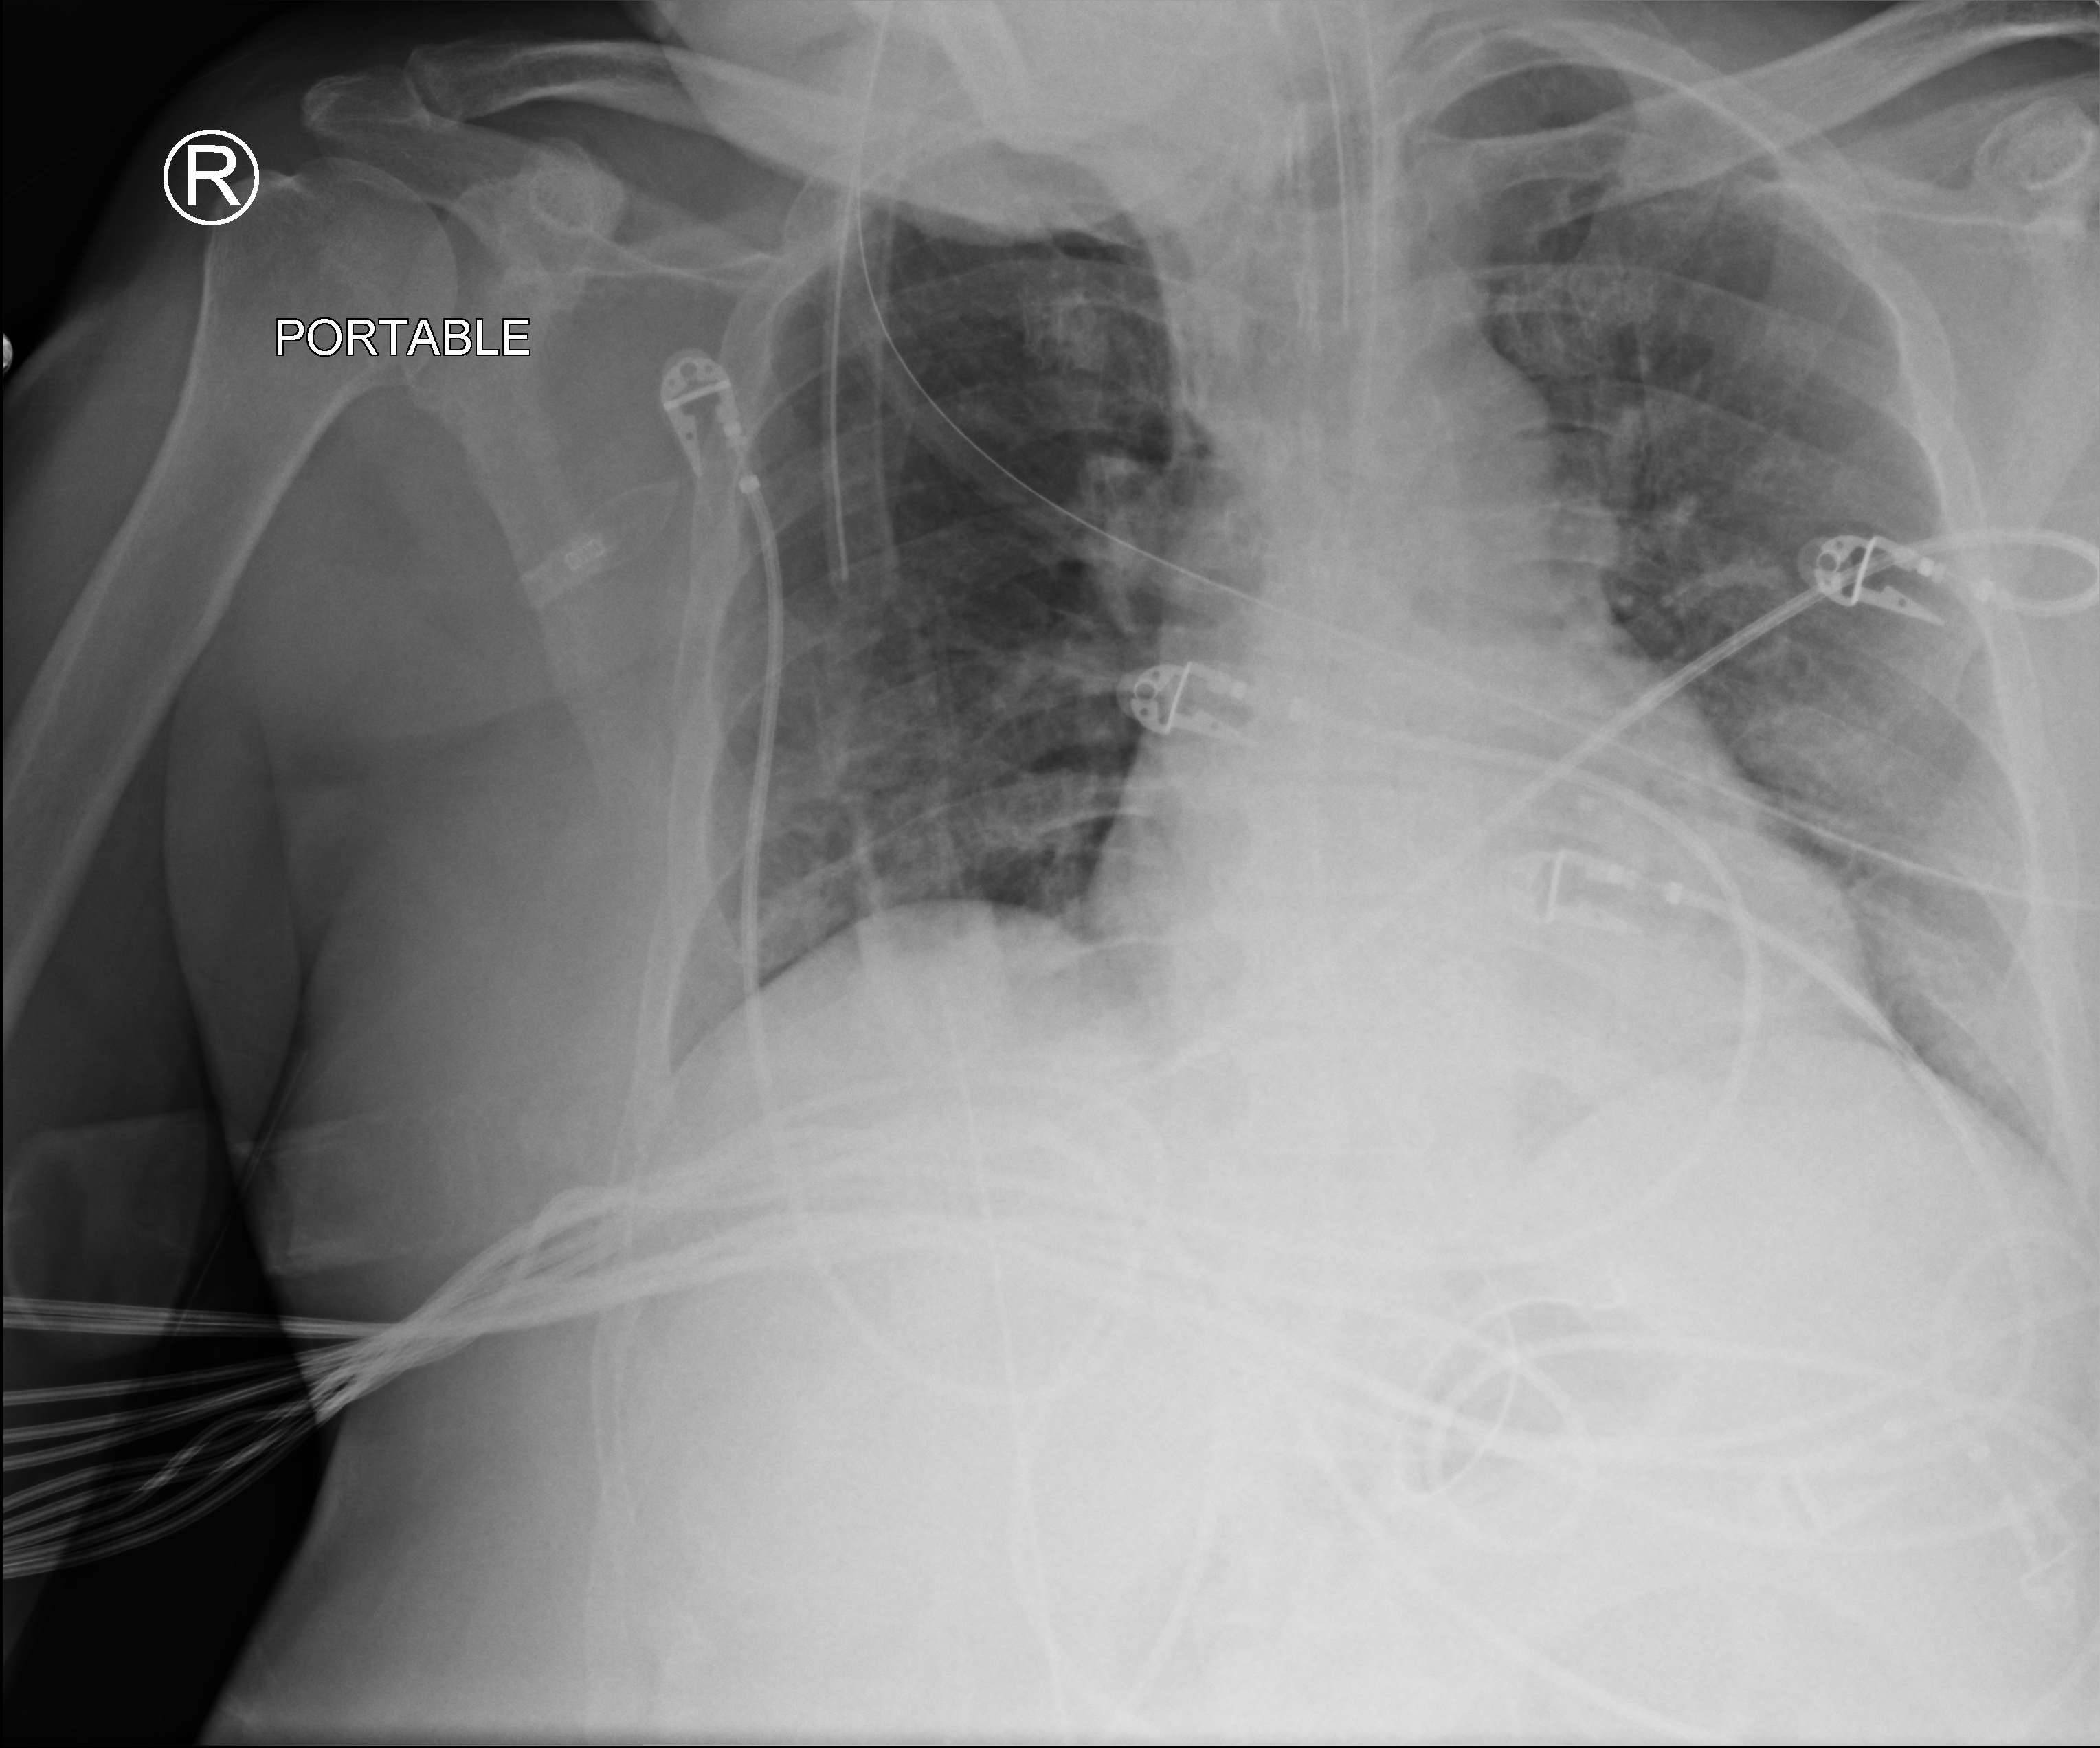
Bedside chest radiograph (computed radiography). Adult patient hospitalised with COVID-19, age 18–59 years.
Admission-level facts for this patient (not findings on this image; timing relative to this image not recorded):
- diabetes (admission record): yes